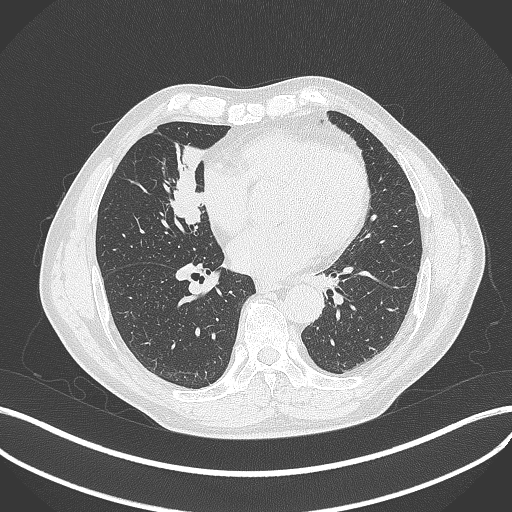
Chest CT, one axial slice; 120 kVp; lung window (W 1500 / L -600 HU); 1 mm slice thickness; 512 × 512 image matrix, field of view 400 × 400 mm. Male patient, age 61 years. Case-level facts recorded for this patient, not image findings: clinical TNM (as recorded): T2b N1 M0.
Outlined on this slice (bounding box drawn by a radiologist):
- lung tumour (recorded histology: squamous cell carcinoma): bounding box (x1, y1, x2, y2) in pixels: (157, 155, 213, 231)